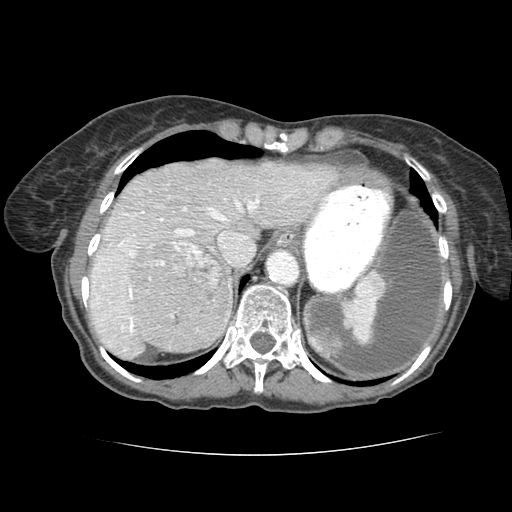
Contrast-enhanced abdominal CT (liver protocol), one axial slice; slice 63 of 77 in the series (ordered by position); reconstruction kernel STANDARD; soft-tissue window (W 400 / L 40 HU); 2.5 mm slice thickness; 512 × 512 image matrix, field of view 340 × 340 mm. Case-level facts recorded for this patient, not image findings: diagnosis: hepatocellular carcinoma (patient treated with transarterial chemoembolisation; whether this scan precedes or follows treatment is not stated here); TNM stage (as recorded): Stage-I; Child-Pugh class: A; tumour differentiation: well differentiated; tumour nodularity: uninodular.
Annotated regions visible in this slice (semi-automatically segmented with operator editing):
- liver parenchyma outside the tumour (the mass and vessels are separate outlines, so this box may not span the whole liver): bounding box <84,158,331,352> (left, top, right, bottom; pixels)
- mass: <128,241,227,346>
- liver vessels: <96,179,301,331>